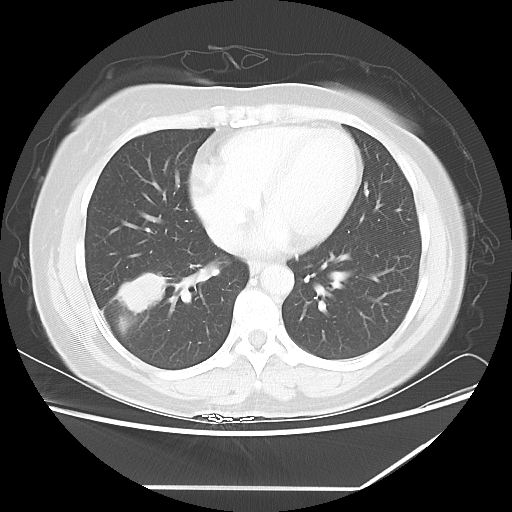
Chest CT, one axial slice. Position 25 of 60 along the scan axis. Reconstruction kernel LUNG. 100 kVp. Lung window (W 1500 / L -600 HU). 5 mm slice thickness. 512 × 512 image matrix. Female patient, age 42 years. Case-level facts recorded for this patient, not image findings: clinical TNM (as recorded): T2 N1 M0.
Outlined on this slice (rectangle marked by the reading radiologist):
- lung tumour (recorded histology: adenocarcinoma): bounding box [x1, y1, x2, y2] px = [113, 270, 166, 317]